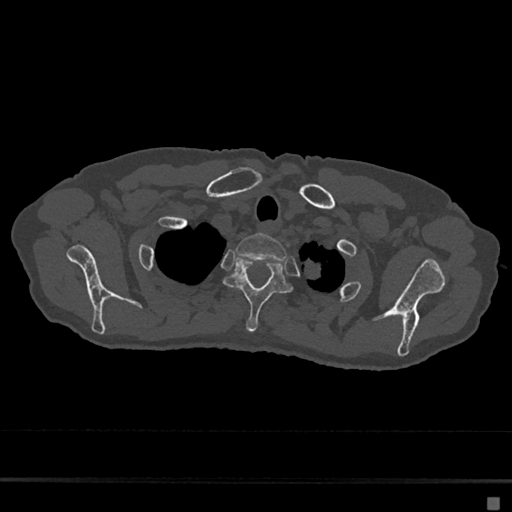
CT including the spine, one axial slice. Position 580 of 797 along the scan axis. 120 kVp. Bone window (W 1800 / L 400 HU). 0.5 mm slice thickness. 512 × 512 image matrix. Patient: female, 68 years. Case-level facts recorded for this patient, not image findings: primary cancer: renal.
Outlined on this slice (semi-automatic segmentation, software-assisted and operator-edited):
- T1 vertebra: box from (x=236, y=233) to (x=287, y=262) px
- T2 vertebra: (x=224, y=255)–(x=292, y=332)